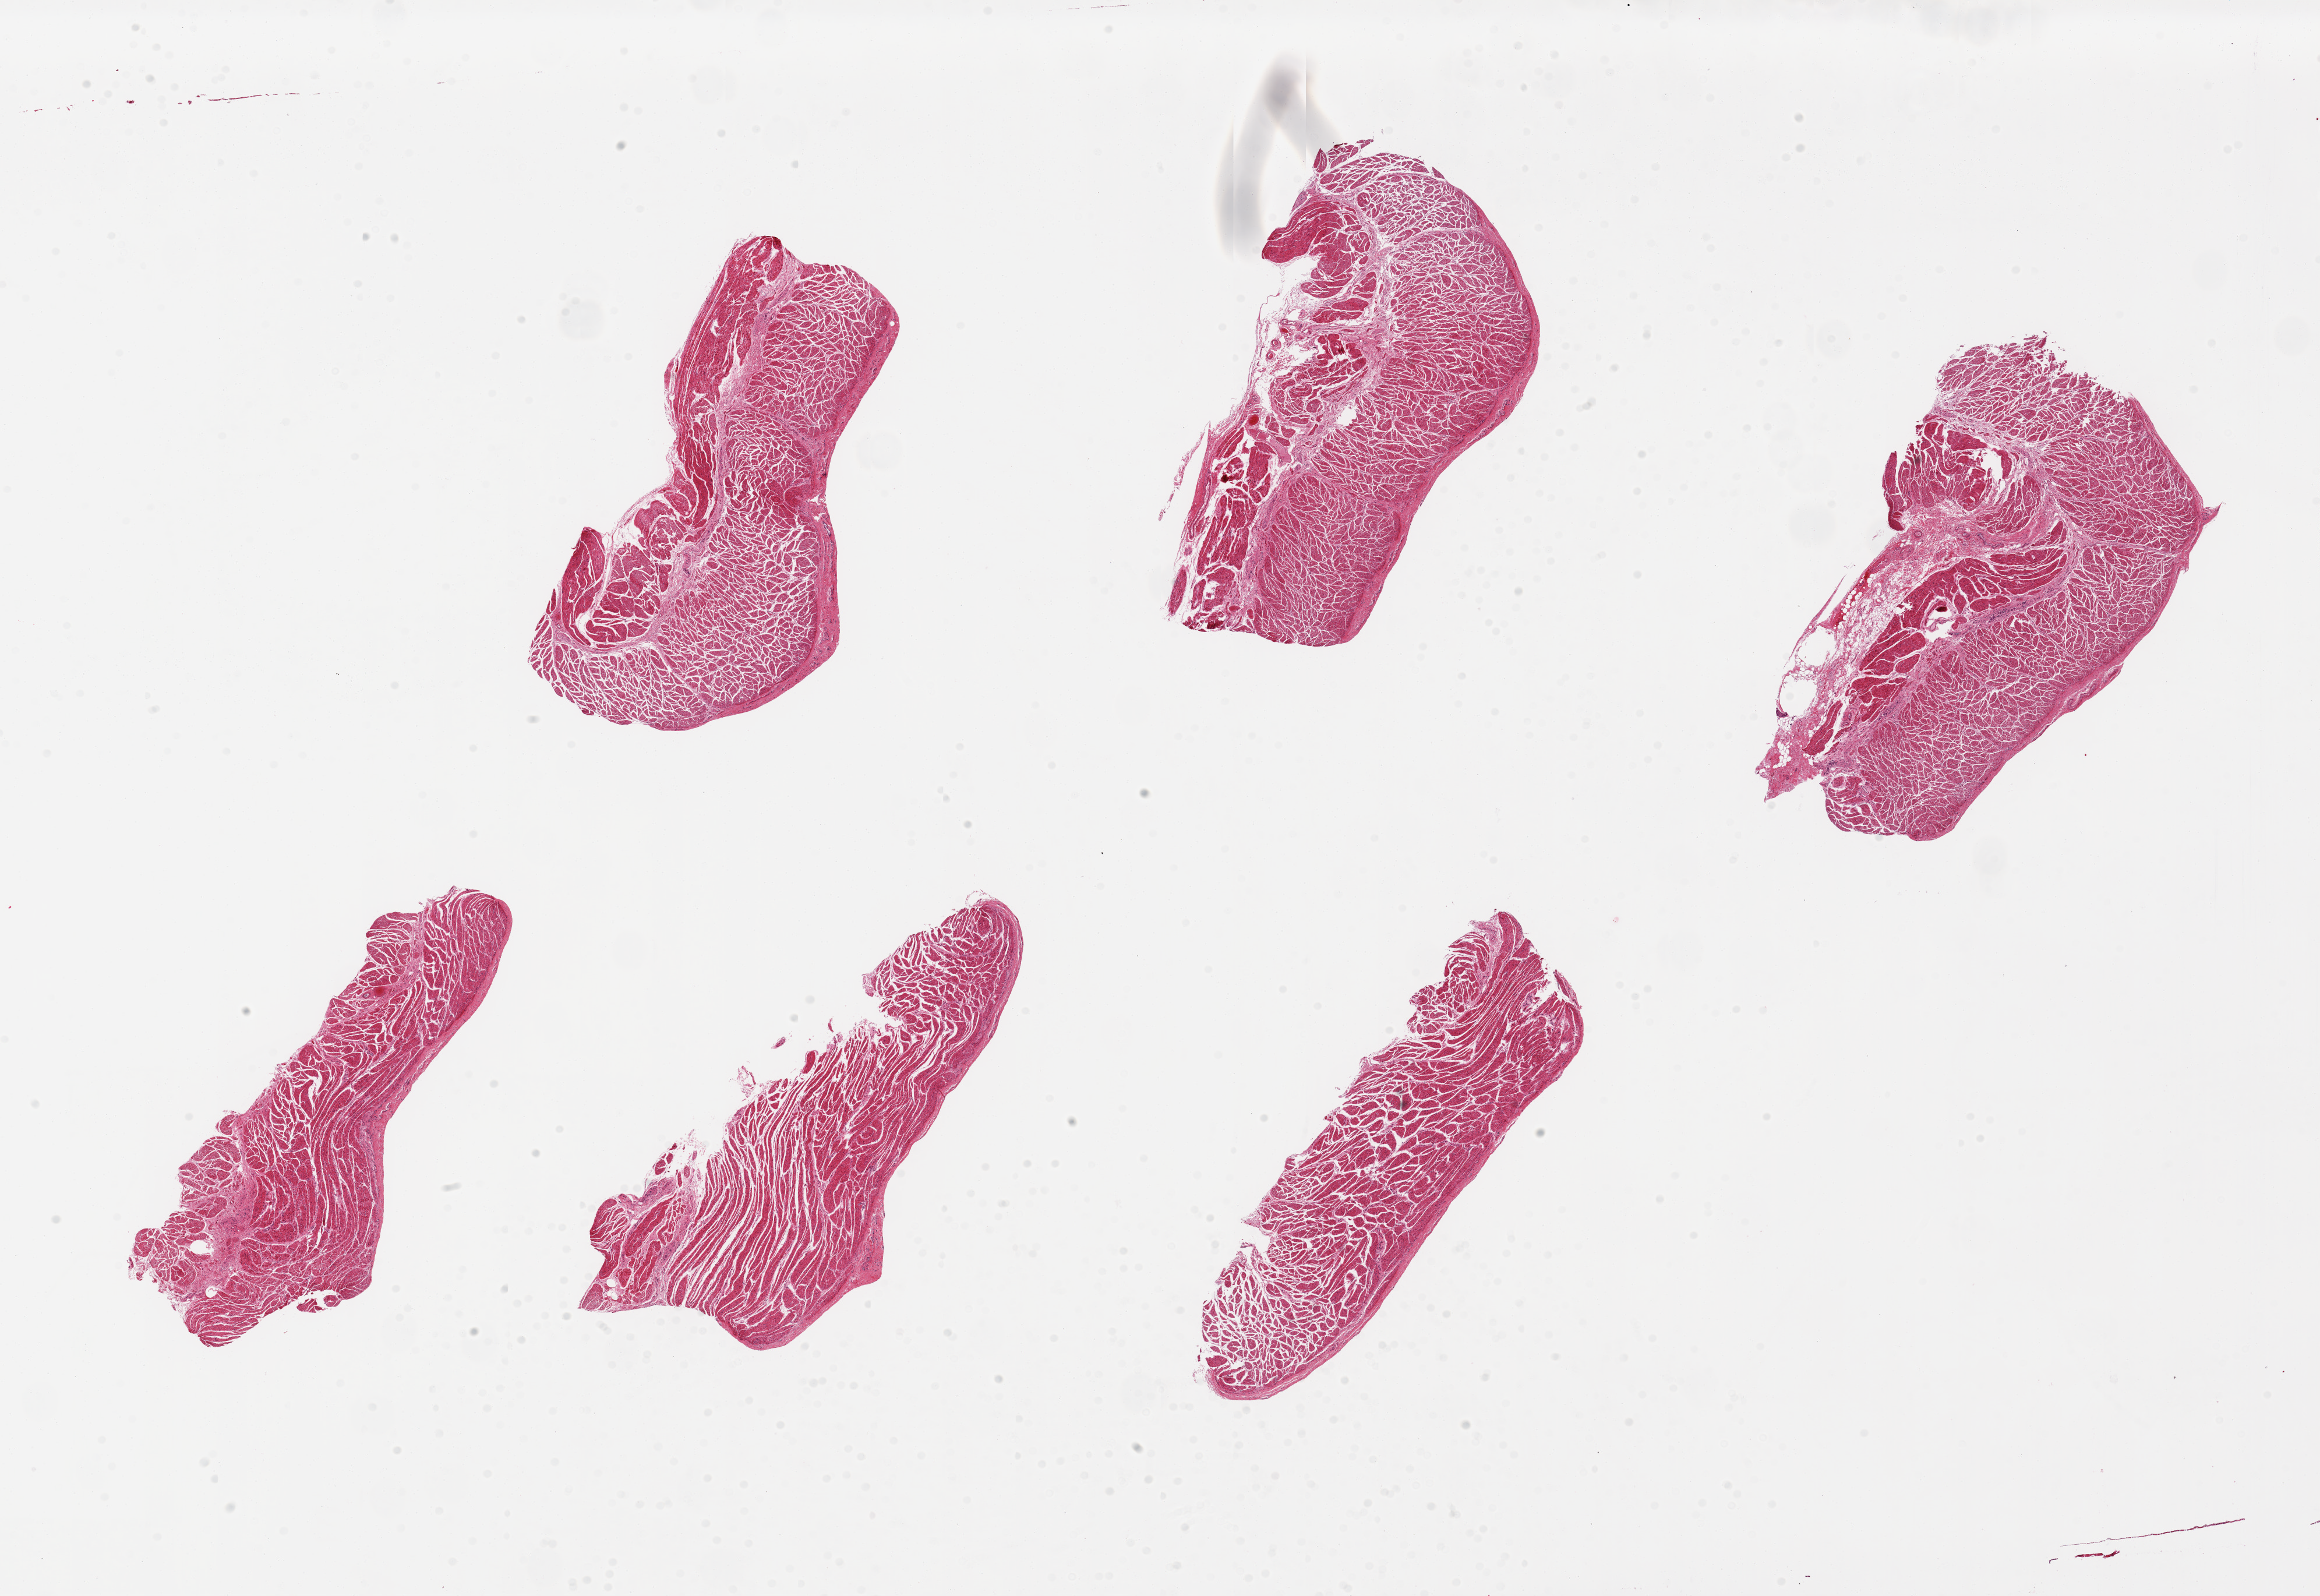
Hematoxylin and eosin (H&E) whole-slide image — whole scanned area (about 31.5 x 21.7 mm, from a 20x scan) shown as a low-resolution overview, PAXgene-fixed paraffin-embedded (PFPE) section, section of esophageal muscle (target tissue), donor tissue sample. Donor: female.
Reviewer comment on this tissue sample: 6 pieces. up to 8x3.5mm; well dissected muscle.